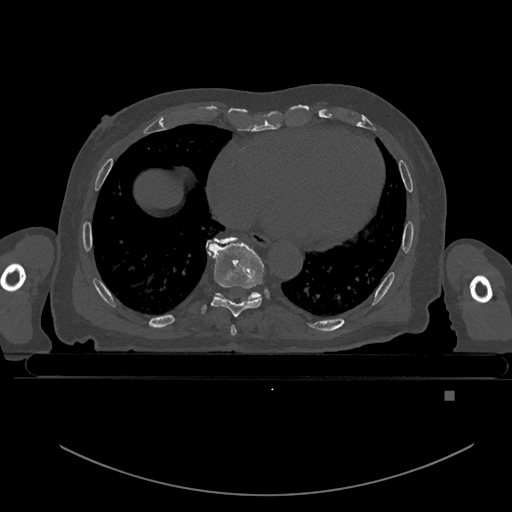
CT including the spine, one axial slice; slice 192 of 969 in the series (ordered by position); bone window (W 1800 / L 400 HU); 512 × 512 image matrix, field of view 456 × 456 mm. Patient: male, 82 years. From the clinical record (not read from this slice): primary cancer: prostate.
Outlined on this slice (semi-automatic segmentation, software-assisted and operator-edited):
- T7 vertebra: box from (x=231, y=325) to (x=237, y=336) px
- T8 vertebra: (x=200, y=238)–(x=264, y=317)
- T9 vertebra: (x=206, y=237)–(x=261, y=301)